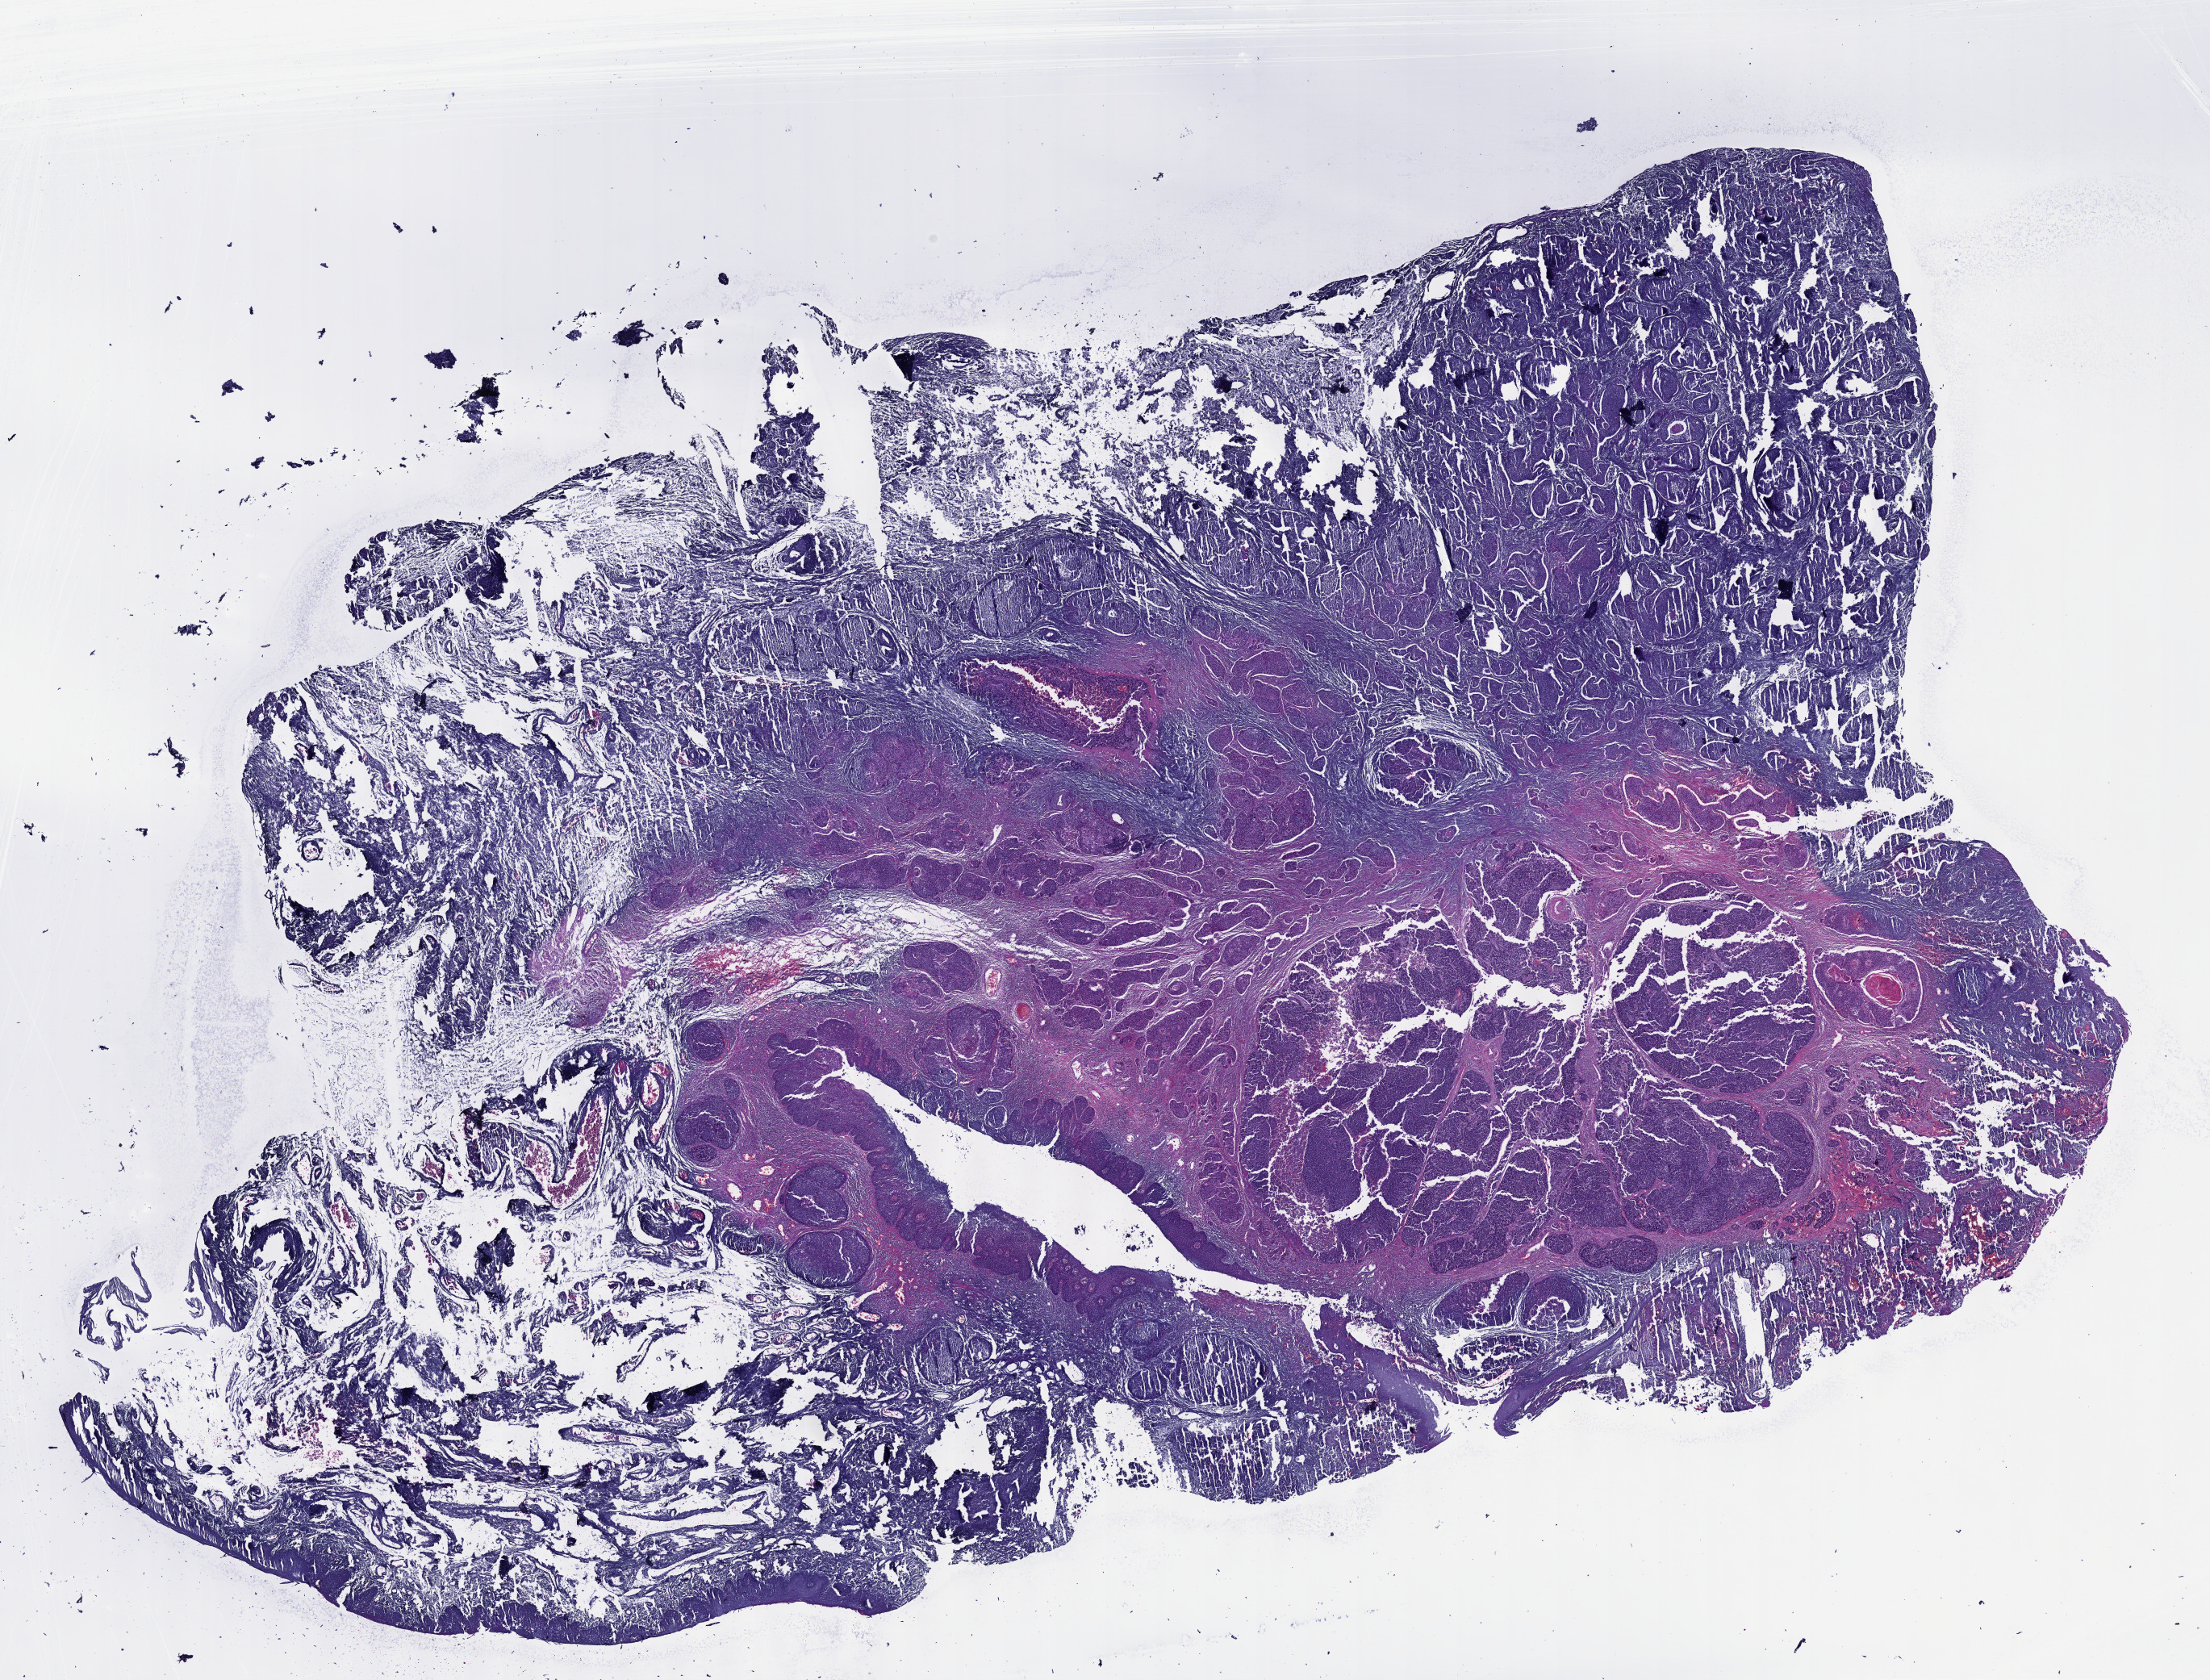
H&E whole-slide image — shown as a low-resolution overview of the whole scanned area (about 22.1 x 16.8 mm), formalin-fixed paraffin-embedded (FFPE) diagnostic section, sample: primary tumour, head and neck. Male patient; age at initial diagnosis 61 years. Histologic grade: G3 (poorly differentiated).
- diagnosis: Squamous cell carcinoma, NOS (larynx, NOS)
- AJCC pathologic stage: IVA (7th edition)